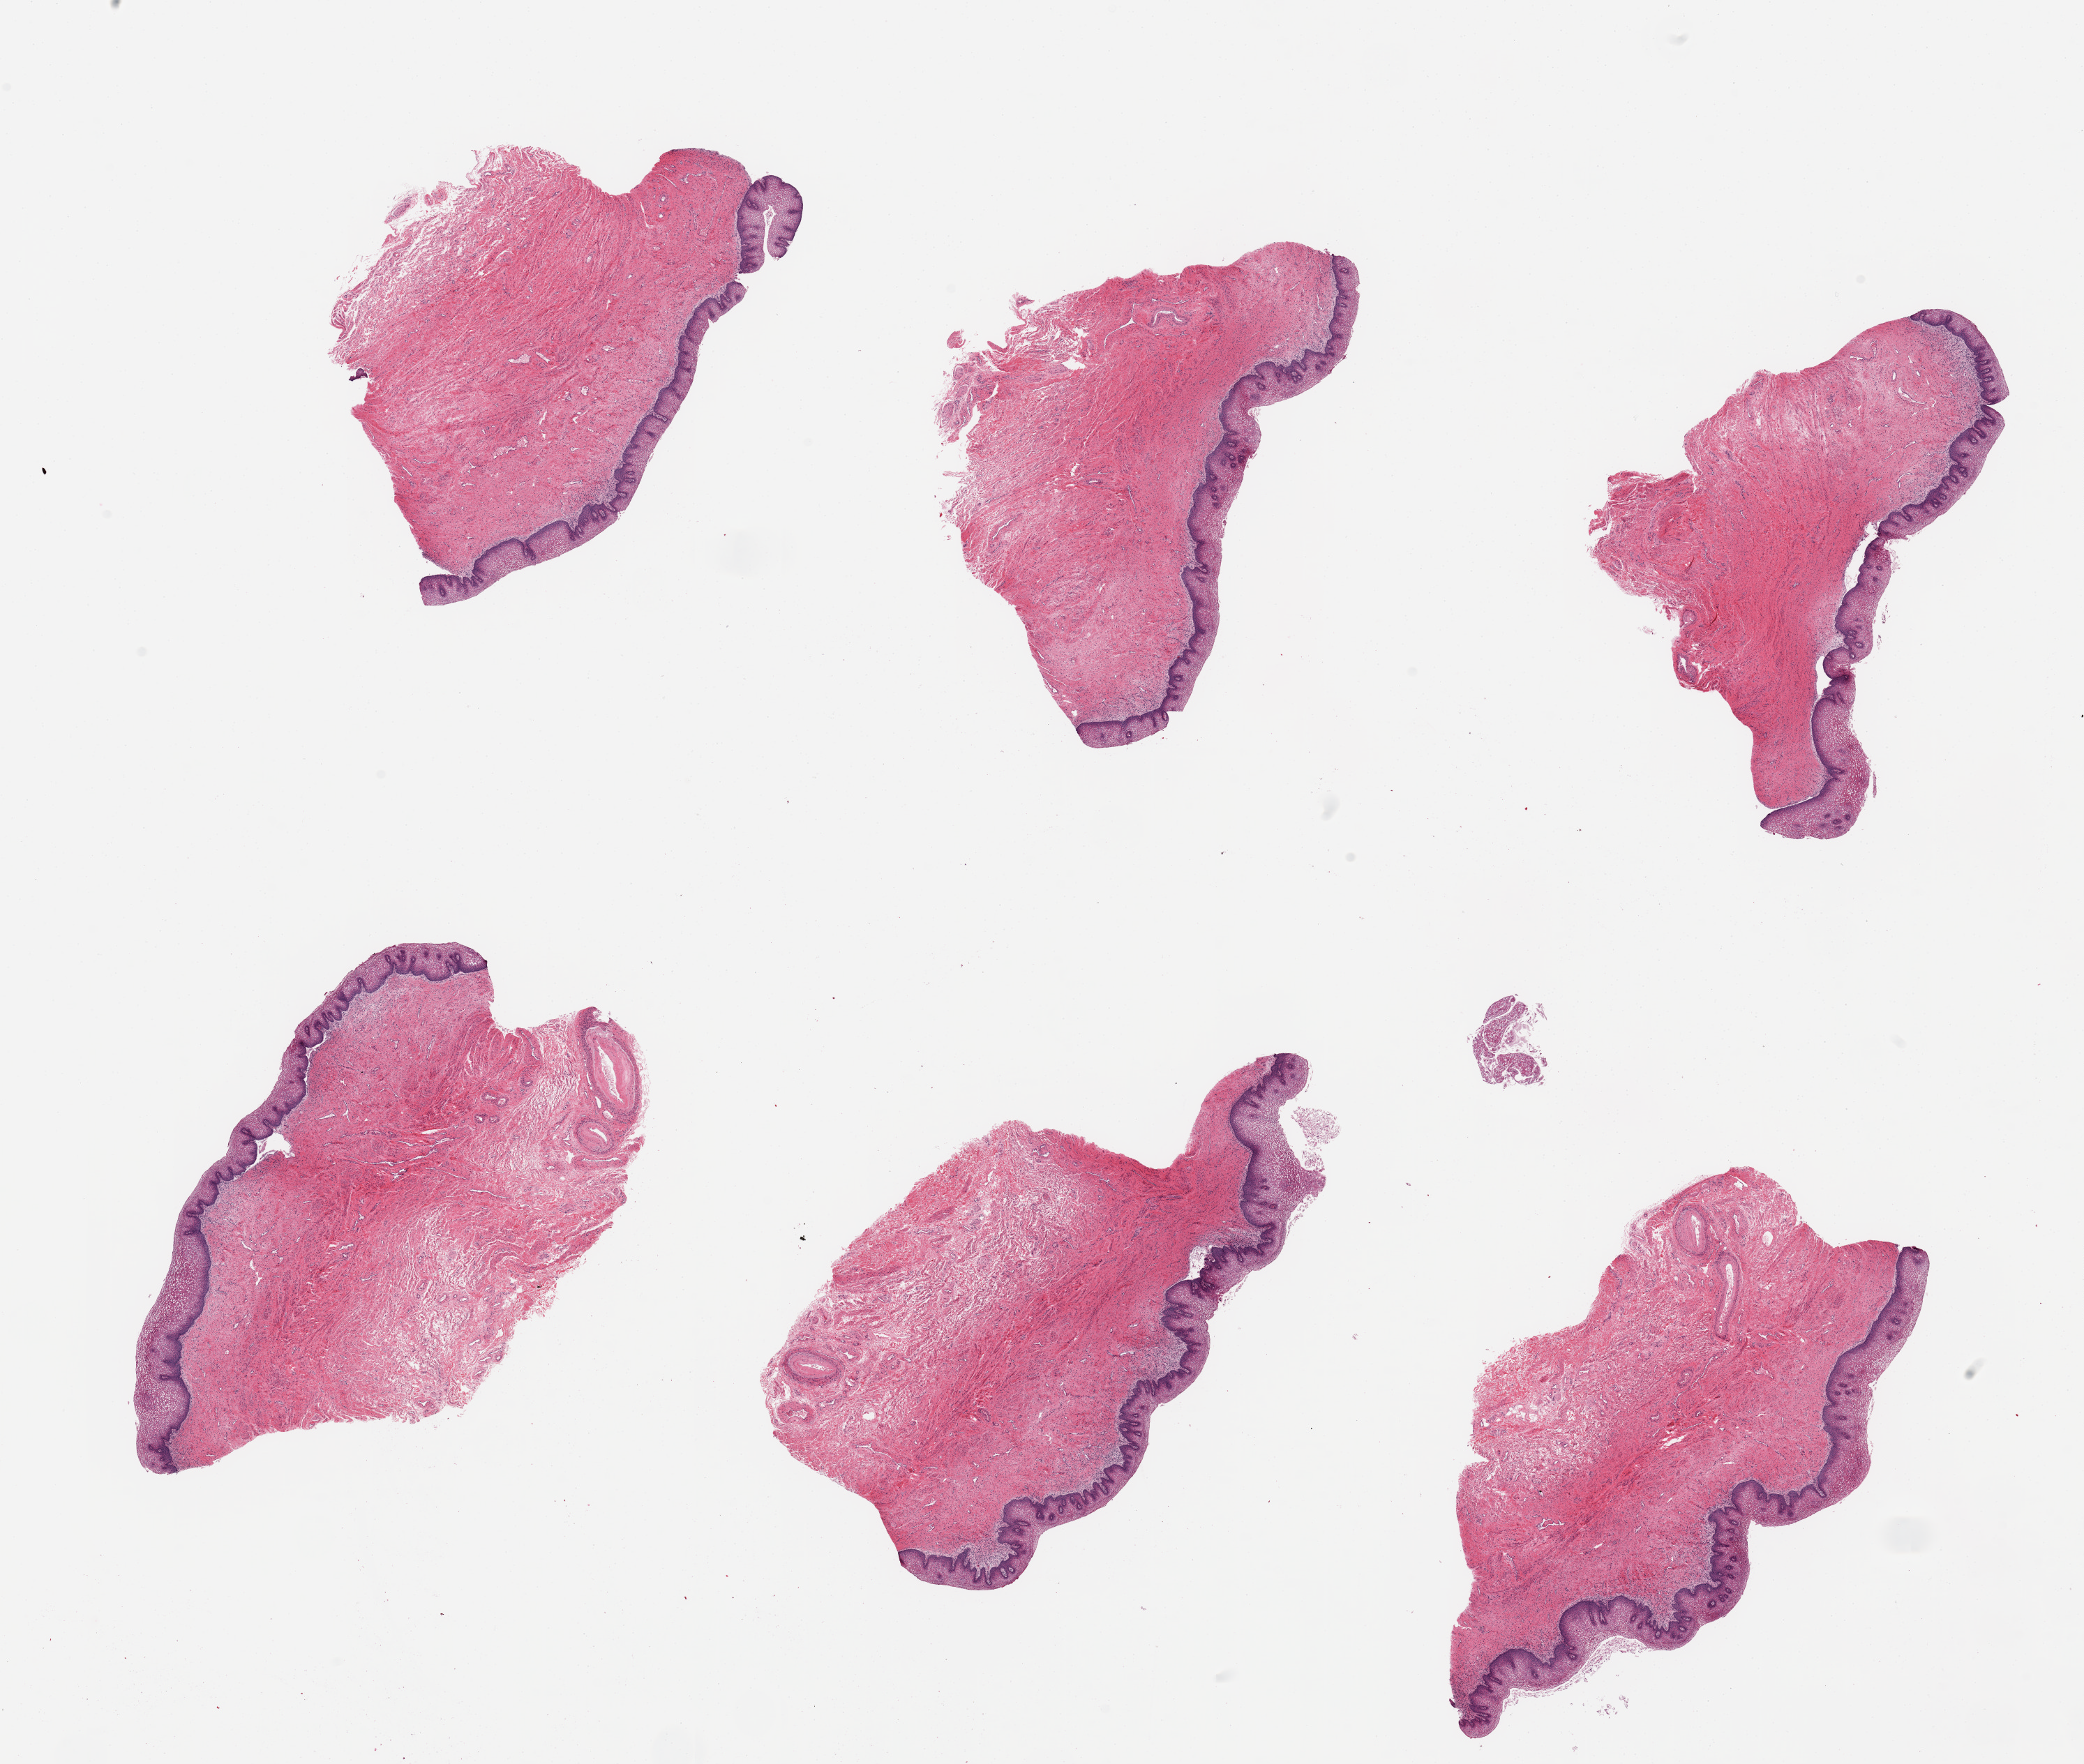
Whole-slide image, hematoxylin and eosin (H&E) stain — low-resolution overview of the scanned area, about 23.6 x 20.0 mm, PAXgene-fixed paraffin-embedded (PFPE) section, target tissue: vagina, donor tissue sample. Donor sex: female.
Pathologist's review note for this sample: 6 pieces.